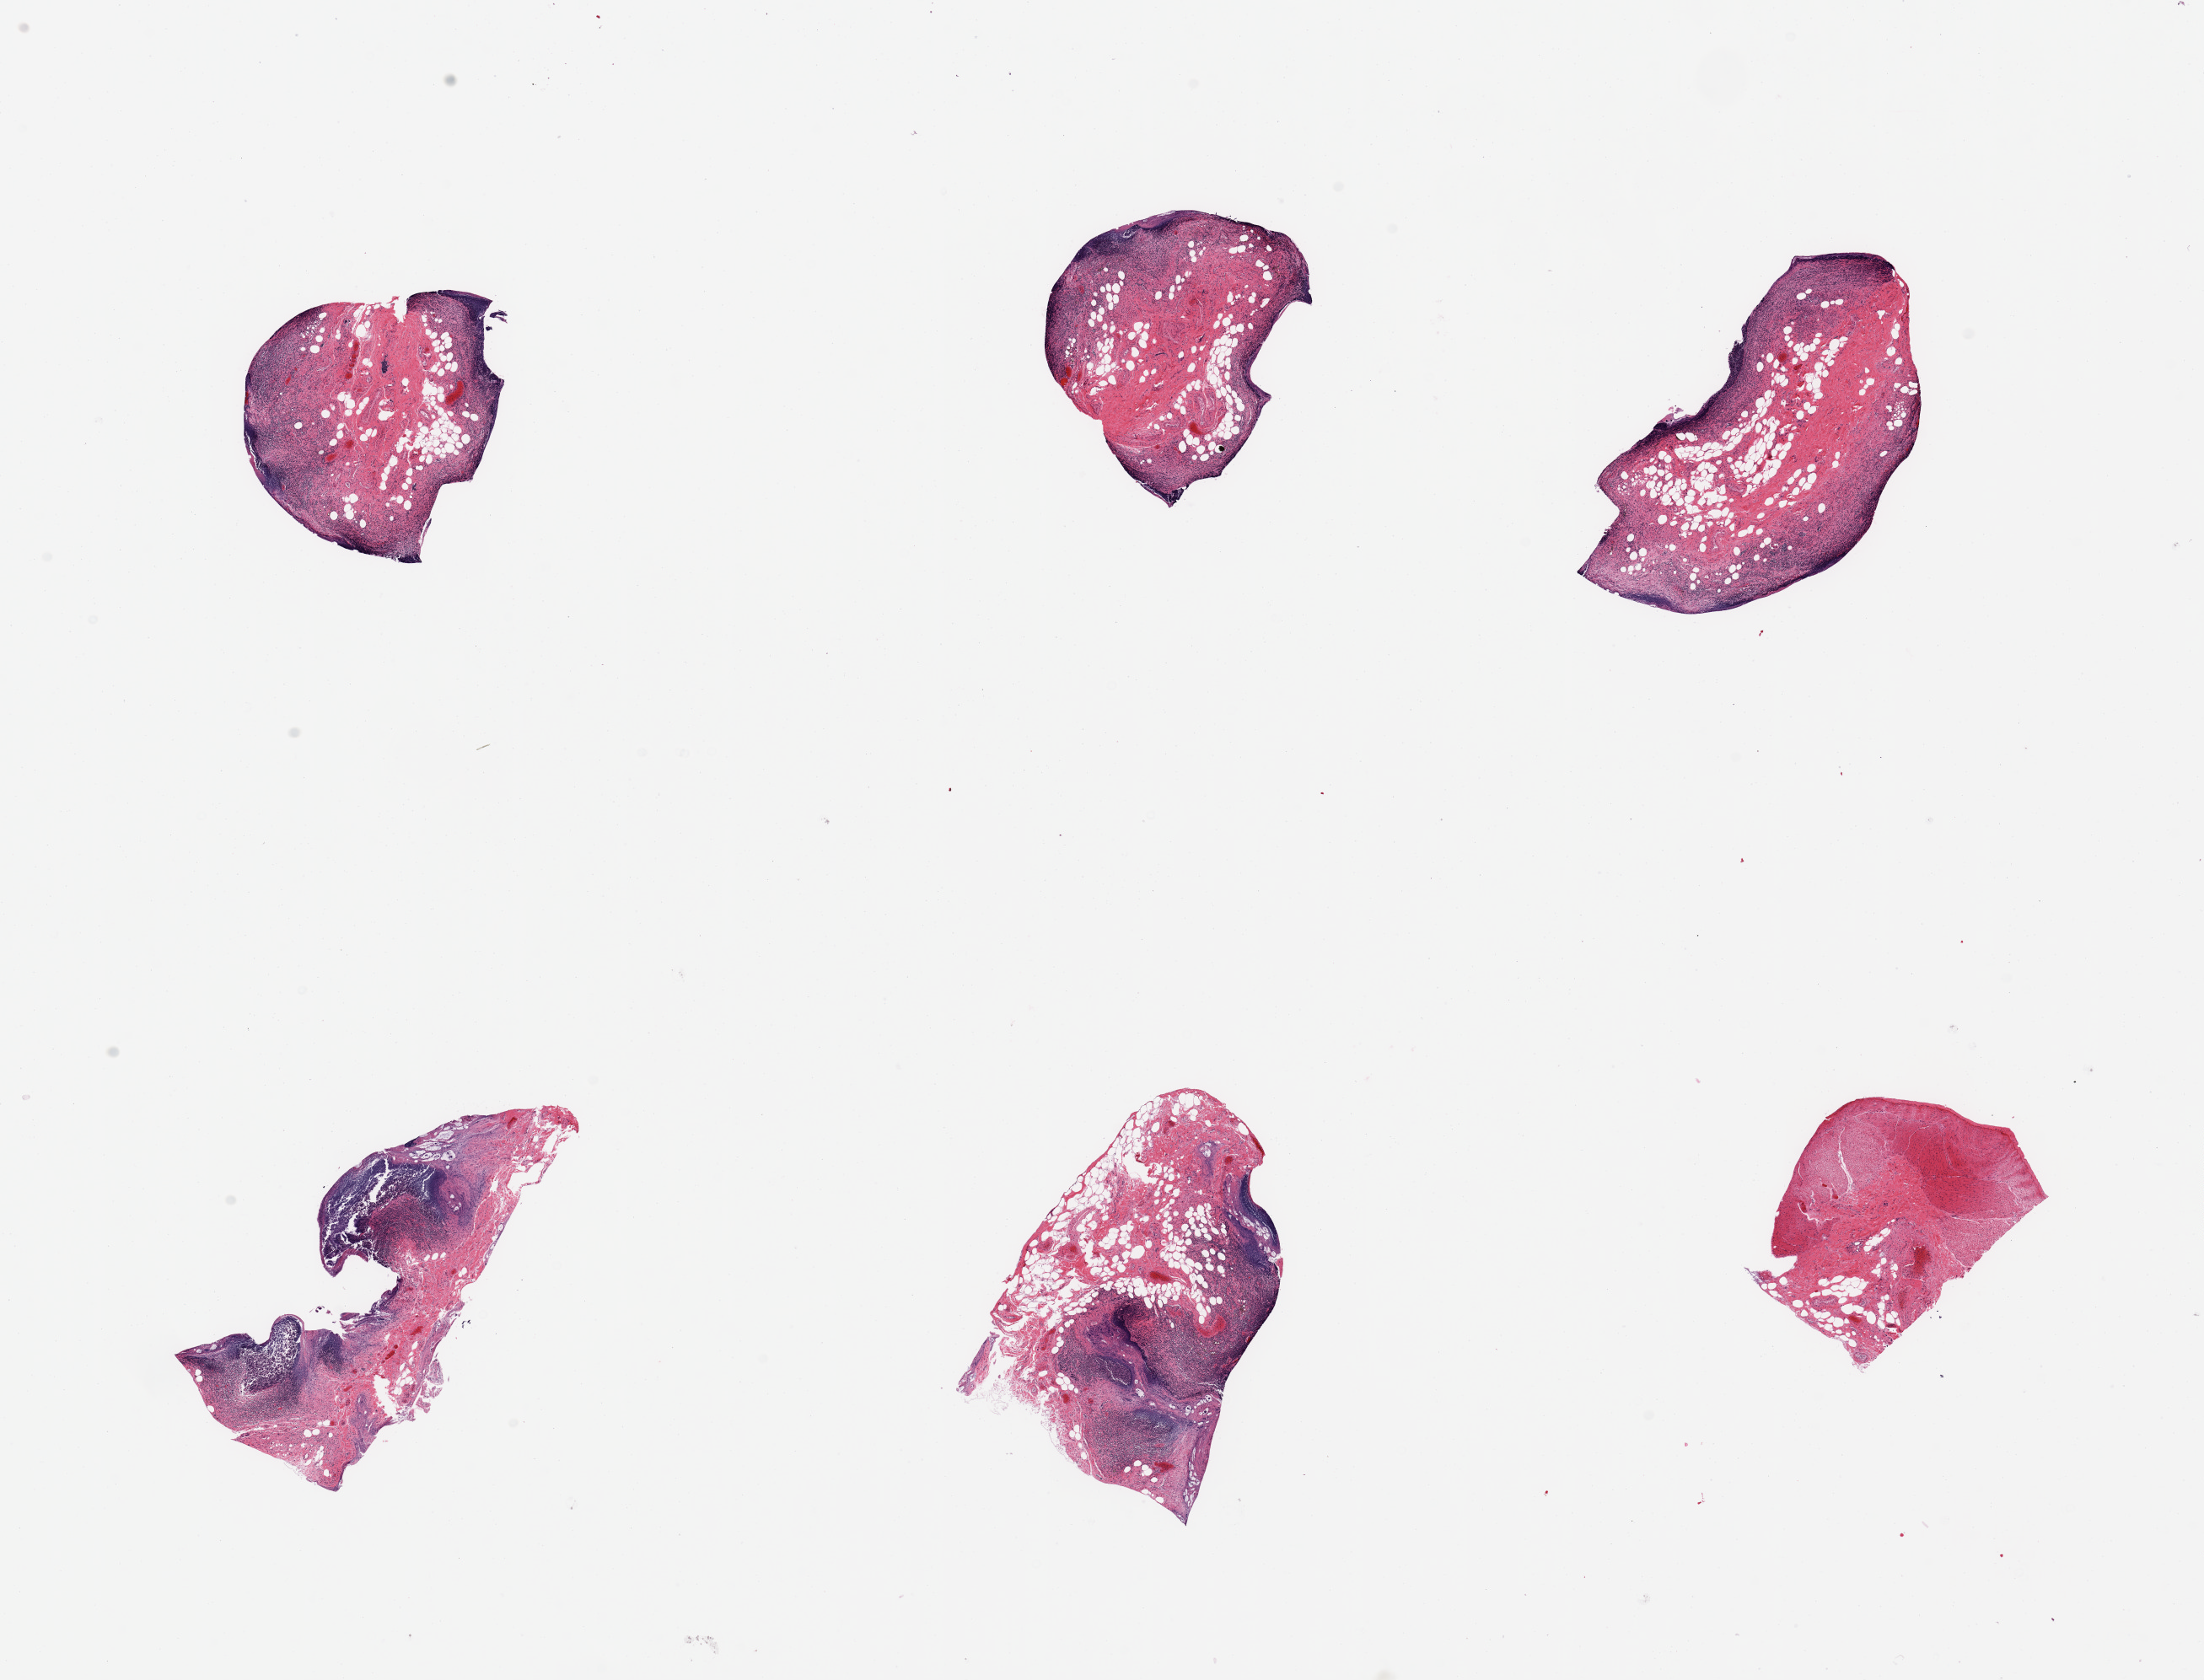
Digitized hematoxylin and eosin (H&E)-stained section, whole scanned area (about 20.7 x 15.8 mm, acquisition: 20x scan) shown as a low-resolution overview. PAXgene-fixed, paraffin-embedded tissue. Sampled site (target tissue): ileum. Donor tissue sample.
• review note (as recorded): 2 pieces; moderately to severely autolyzed, but with significant lymphoid component in 5 of 6 pieces, one piece is muscularis only